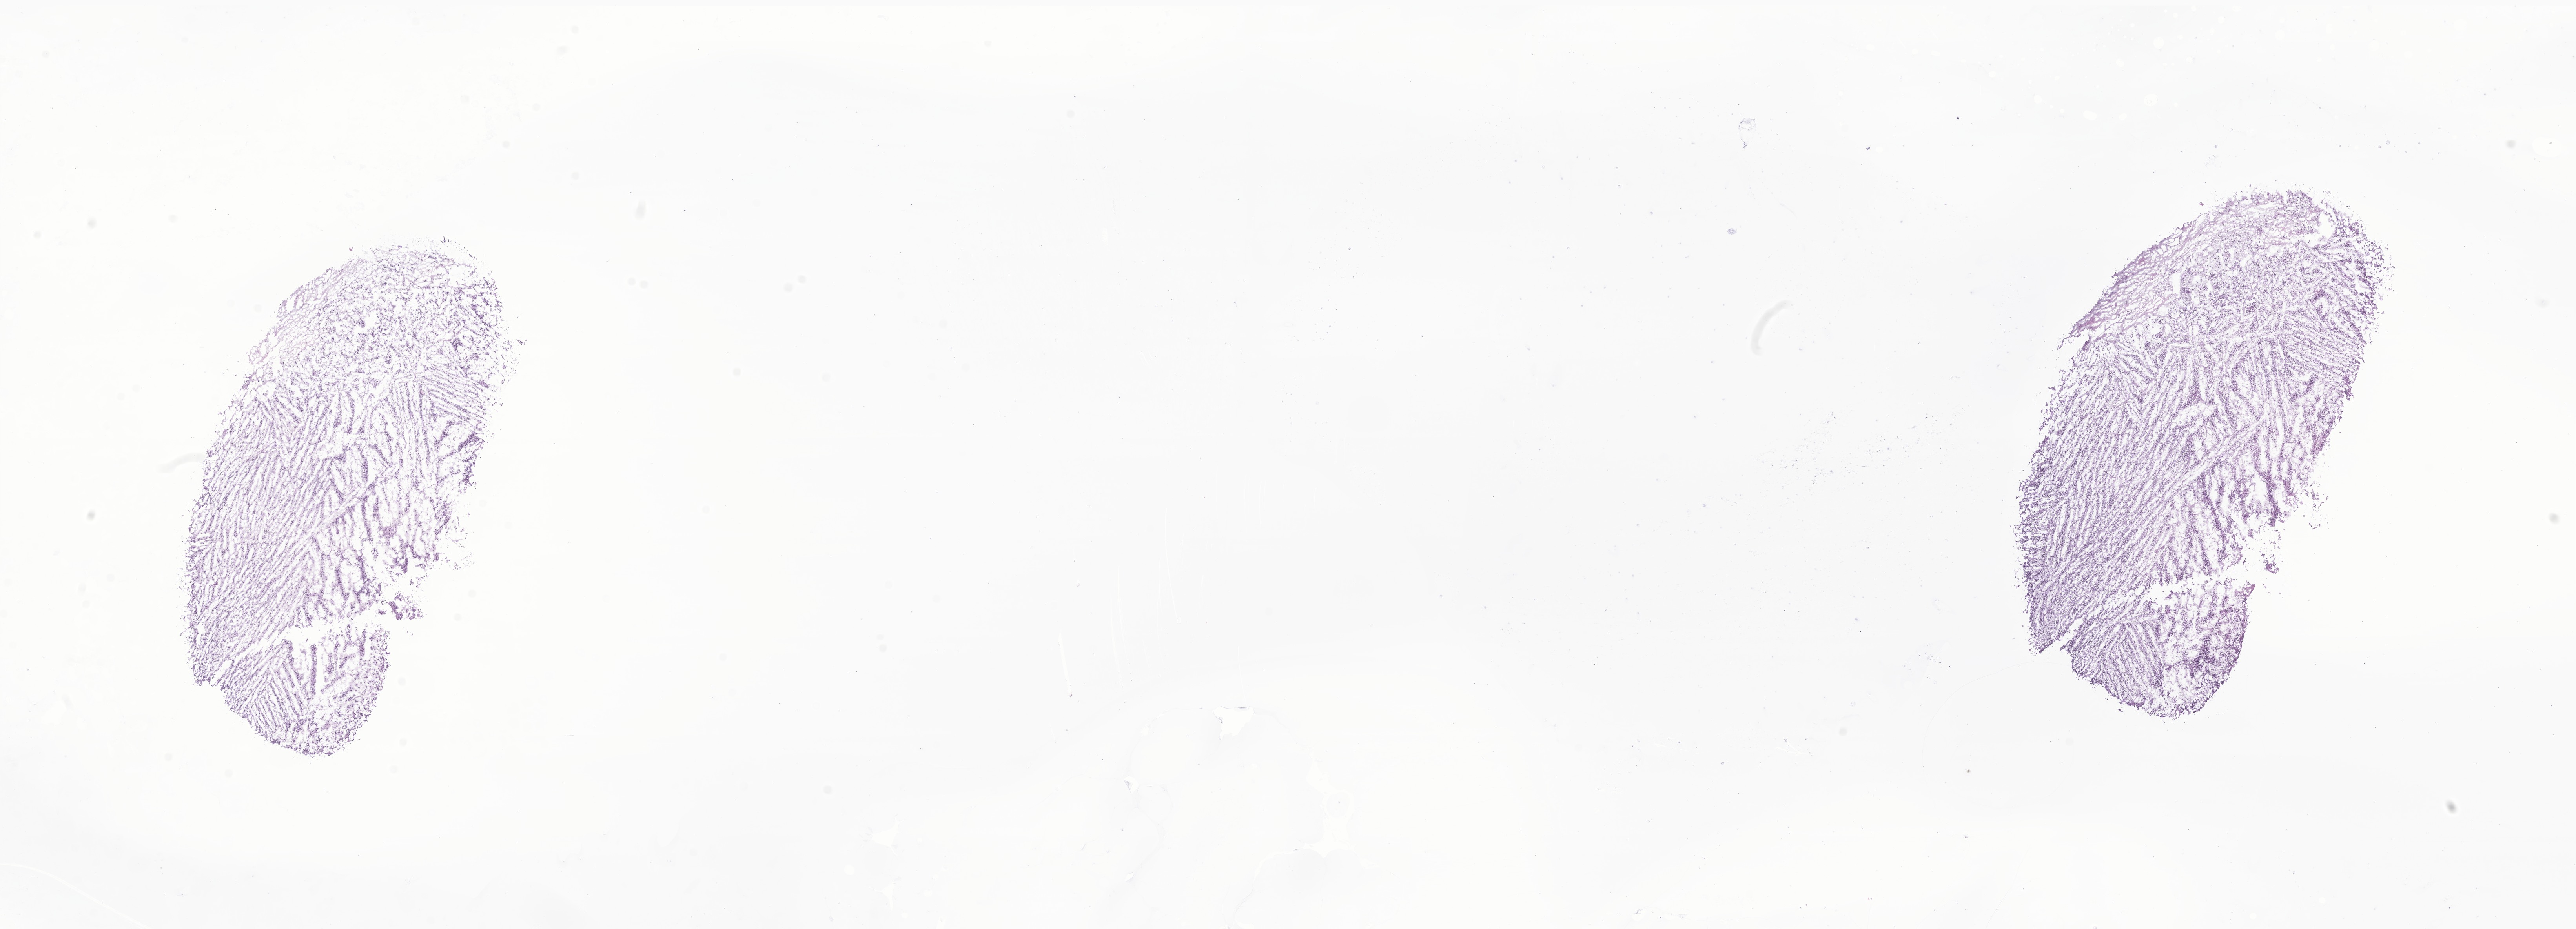
Digitized hematoxylin and eosin (H&E)-stained section of tumor tissue from the adrenal gland, a low-resolution overview of the entire scanned area, about 27.7 x 10.0 mm. Cryosection (OCT / tissue freezing medium). Male patient, age 502 days.
Diagnosis: Neuroblastoma, NOS.